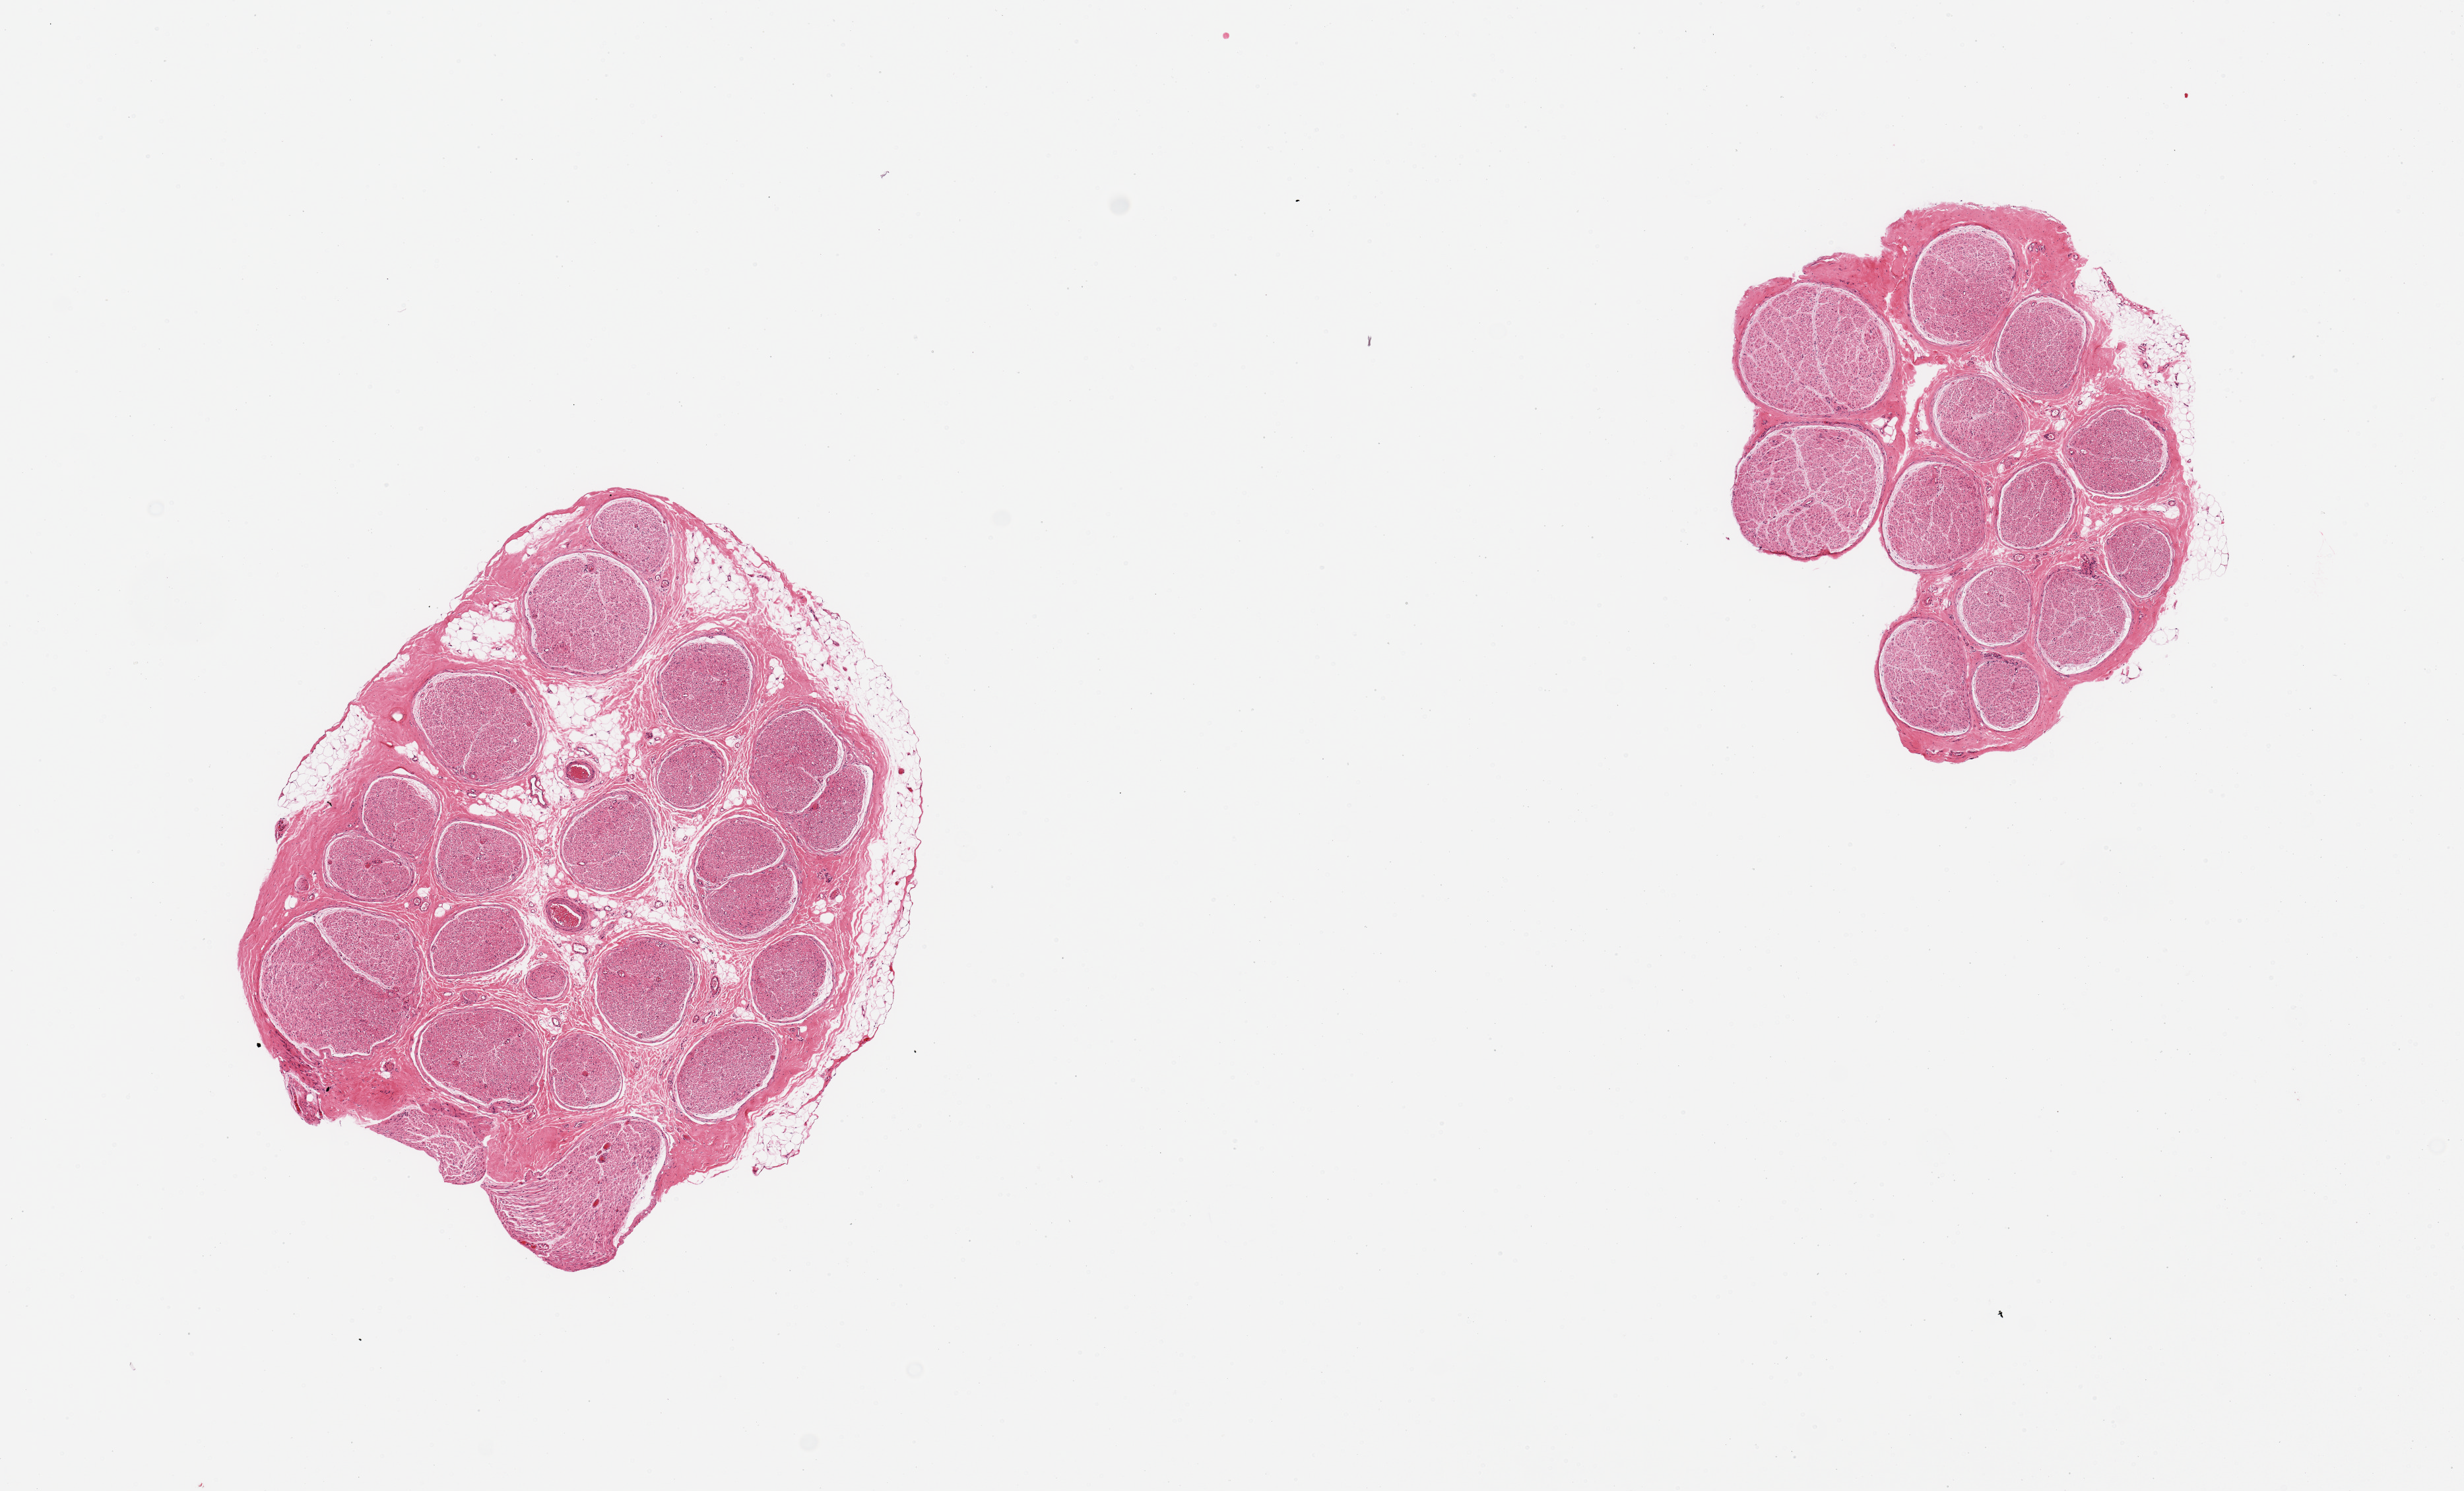
Haematoxylin and eosin whole-slide image — shown as a low-resolution overview of the whole scanned area (about 14.8 x 8.9 mm), PAXgene-fixed, paraffin-embedded tissue, section of tibial nerve (target tissue), donor tissue sample. Donor: female.
• pathologist's review note for this sample: 2 pieces, trace adherent fat up to ~0.2mm focally